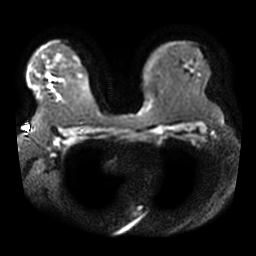
Breast MRI, one axial slice. Position 29 of 42 along the scan axis. Diffusion-weighted series; image 2 of 4 stored at this slice position (different b-values; order by instance number). 3 T. 256 × 256 image matrix. Female patient.
Outlined on this slice (manually delineated by an expert):
- tumour on diffusion-weighted imaging: bounding box <48,76,53,80> (left, top, right, bottom; pixels)